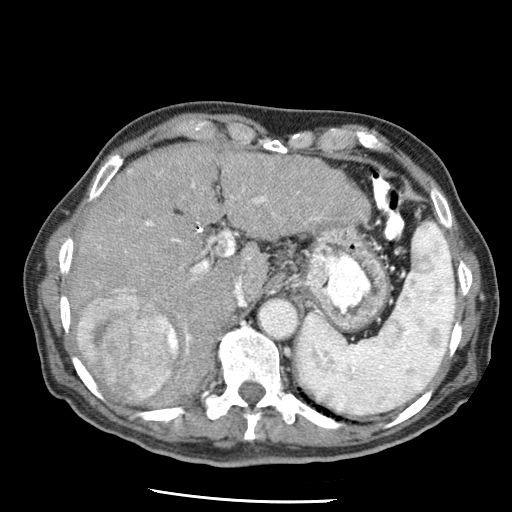
Contrast-enhanced abdominal CT (liver protocol), one axial slice. Slice 43 of 79 in the series (ordered by position). Soft-tissue window (W 400 / L 40 HU). 2.5 mm slice thickness. 512 × 512 image matrix, field of view 320 × 320 mm. Case-level facts recorded for this patient, not image findings: diagnosis: hepatocellular carcinoma (patient treated with transarterial chemoembolisation; whether this scan precedes or follows treatment is not stated here); TNM stage (as recorded): Stage-IIIA; Child-Pugh class: A.
Structures marked on this image (semi-automatic segmentation, software-assisted and operator-edited):
- liver parenchyma outside the tumour (the mass and vessels are separate outlines, so this box may not span the whole liver): bounding box [x1, y1, x2, y2] px = [70, 144, 370, 402]
- mass: [76, 293, 177, 399]
- liver vessels: [96, 170, 321, 292]